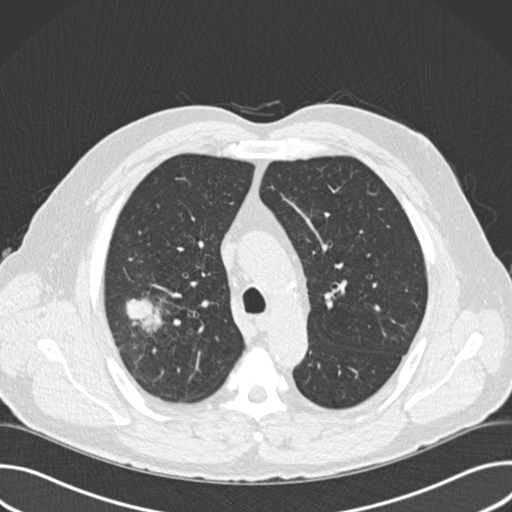
Low-dose screening chest CT, one axial slice; position 115 of 157 along the scan axis; lung window (W 1500 / L -600 HU); 512 × 512 image matrix.
Structures marked on this image (outlined manually by an expert reader):
- lesion 1 (tumor, upper lobe of right lung): bounding box [x1, y1, x2, y2] px = [126, 298, 162, 332]